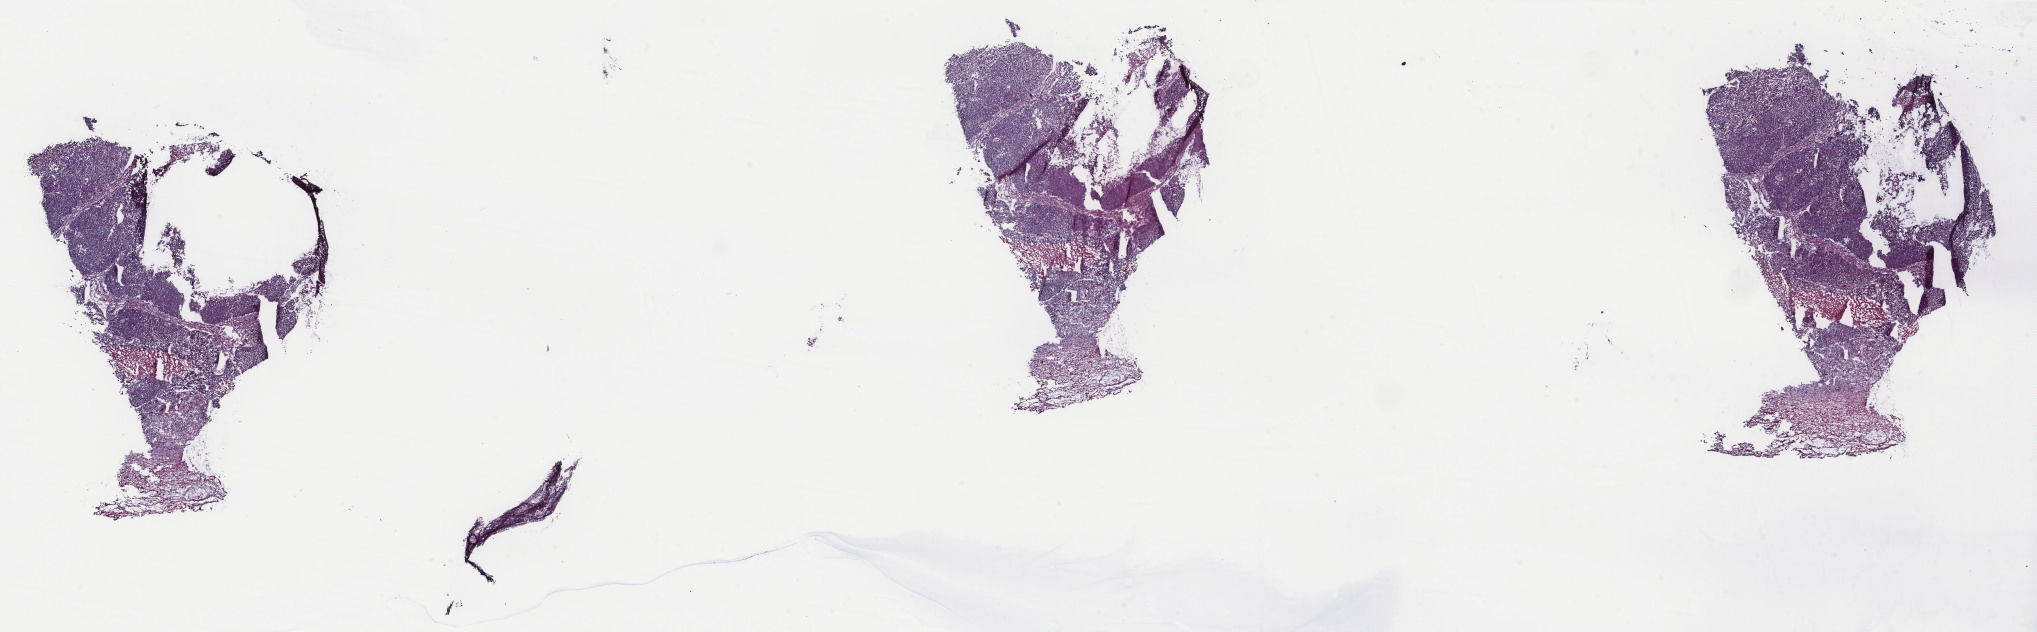
H&E-stained whole-slide image, whole scanned area (about 32.3 x 10.0 mm, slide scanned at 40x) shown as a low-resolution overview; frozen section from the top of the tissue portion; sample: primary tumour, lung. Female patient; age at initial diagnosis 75 years. Slide review estimates, as recorded: tumour cells 85%, tumour nuclei 92%, normal cells 0%, stromal cells 5%, necrosis 10%. Inflammatory infiltration, as recorded: lymphocyte infiltration 0%, monocyte infiltration 0%, neutrophil infiltration 0%.
Pathologic diagnosis: Basaloid squamous cell carcinoma. Laterality: right. AJCC pathologic stage: IIA (7th edition).